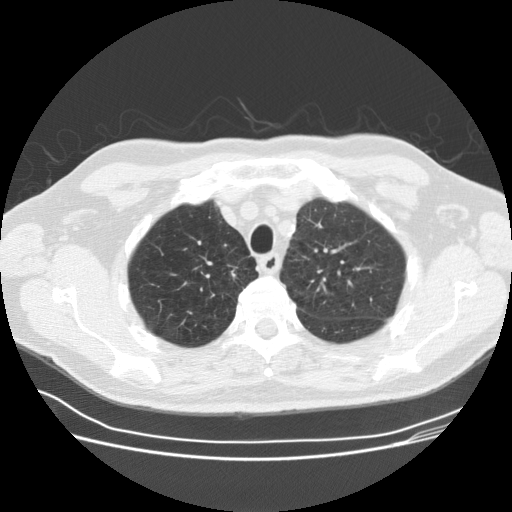
Low-dose screening chest CT, one axial slice. Slice 129 of 164 in the series (ordered by position). Lung window (W 1500 / L -600 HU). 2.5 mm slice thickness. 512 × 512 image matrix.
Outlined on this slice (outlined manually by an expert reader):
- lesion 1 (tumor, upper lobe of right lung): bounding box (x1, y1, x2, y2) in pixels: (227, 264, 238, 277)